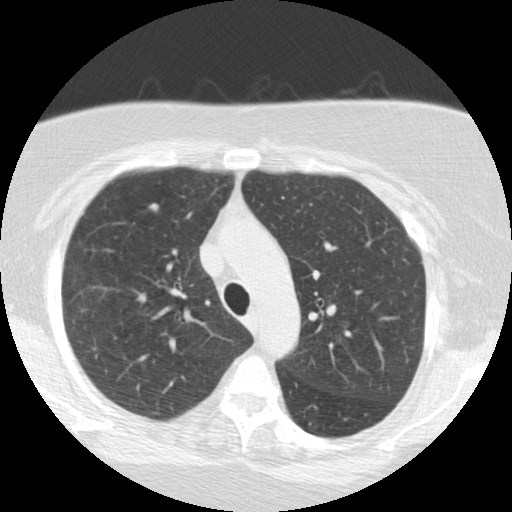
Low-dose screening chest CT, axial slice; second screening round (one year after baseline); lung window (W 1500 / L -600 HU); 2.5 mm slice thickness; standard (soft-tissue) reconstruction kernel (STANDARD); slice 172 of 225 in the series. Female participant, aged 64 years at enrolment.
Lesion marked by an expert reader, bounding box [x1, y1, x2, y2] px = [127, 193, 170, 230]. Screening reader's record for this exam (one nodule recorded; not confirmed to be the boxed lesion): non-calcified nodule or mass ≥4 mm, right upper lobe, 8 × 7 mm, smooth margins, soft tissue attenuation, pre-existing on the prior screen: no. Official screen result: positive, other. Later outcome: lung cancer diagnosed 85 days after this screen — large cell neuroendocrine carcinoma, right upper lobe, stage IA (AJCC 6th edition), 12 mm at pathology.